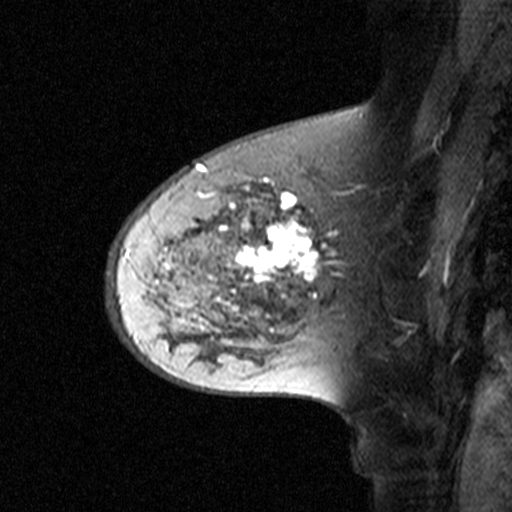
Breast MRI (dynamic contrast-enhanced), one sagittal slice; slice 28 of 44 in the series (ordered by position); dynamic contrast-enhanced study with each time point stored as its own series, time point 2 of 3 at this slice position (early post-contrast, ordered by acquisition time); 1.5 T; TE 4.5 ms, TR 11 ms; 3 mm slice thickness; 512 × 512 image matrix, field of view 200 × 200 mm. Female patient, age 65 years. Case-level facts recorded for this patient, not image findings: setting: breast cancer imaged before/during neoadjuvant chemotherapy; receptor status: HER2-positive.
Outlined on this slice (semi-automatic segmentation, software-assisted and operator-edited):
- analysis volume of interest (the breast-tissue region the enhancement analysis was run in; not a lesion): bounding box (x1, y1, x2, y2) in pixels: (160, 172, 329, 345)
- tumour enhancement mask (voxels above the 90 % enhancement threshold inside the analysis volume of interest): (191, 185, 329, 331)